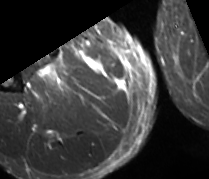
MRI of an extremity soft-tissue mass, one axial slice. Position 22 of 89 along the scan axis. STIR. MR volume resampled by the dataset authors to the PET/CT grid (not the native acquisition matrix). 3.27 mm slice thickness. 209 × 179 image matrix, field of view 204 × 175 mm. Male patient. Case-level facts recorded for this patient, not image findings: histological type: undifferentiated - pleiomorphic; grade: high; site of the primary tumour: right thigh.
Outlined on this slice (expert contour drawn on MRI and transferred to this co-registered scan by the dataset authors):
- gross tumour volume including surrounding oedema: bounding box (x1, y1, x2, y2) in pixels: (39, 62, 67, 86)